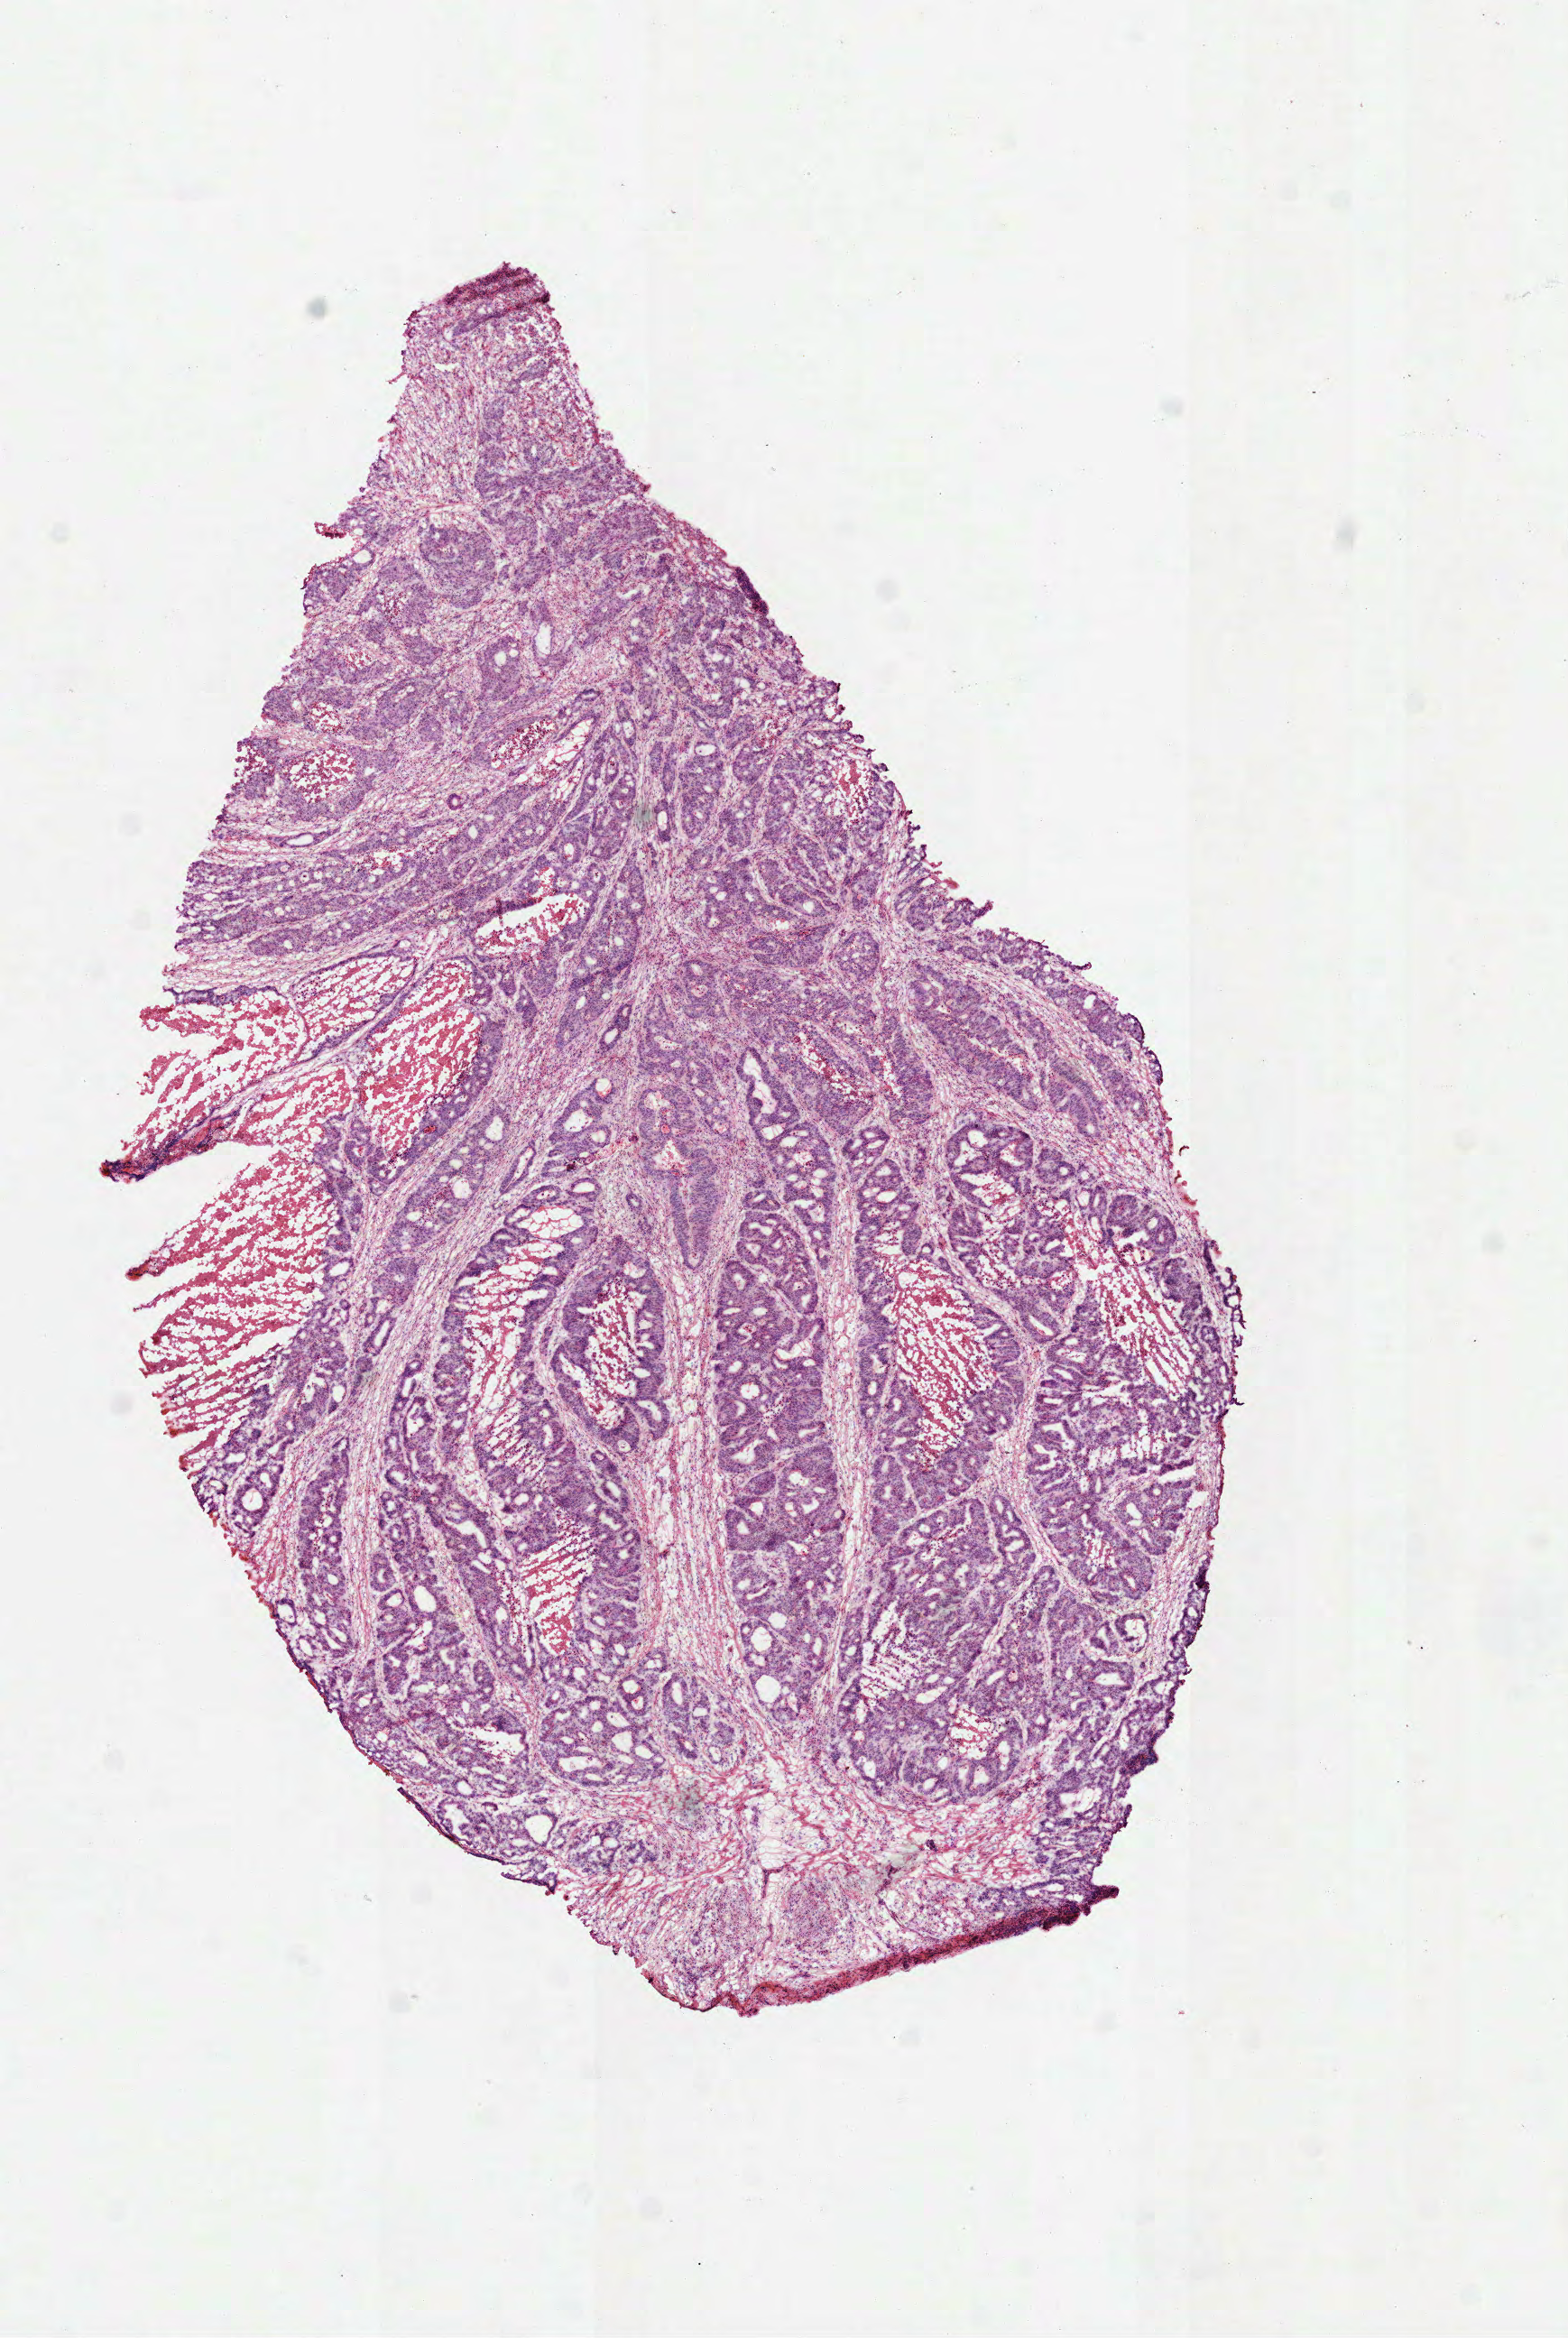
H&E whole-slide image — shown as a low-resolution overview of the whole scanned area (about 7.0 x 10.5 mm), frozen section from the top of the tissue portion, sample: primary tumour, colon. Patient: male, age at initial diagnosis 75 years. Composition of this section per pathologist review: tumour cells 80%, tumour nuclei 80%.
Histologic diagnosis: Adenocarcinoma, NOS (hepatic flexure of colon).